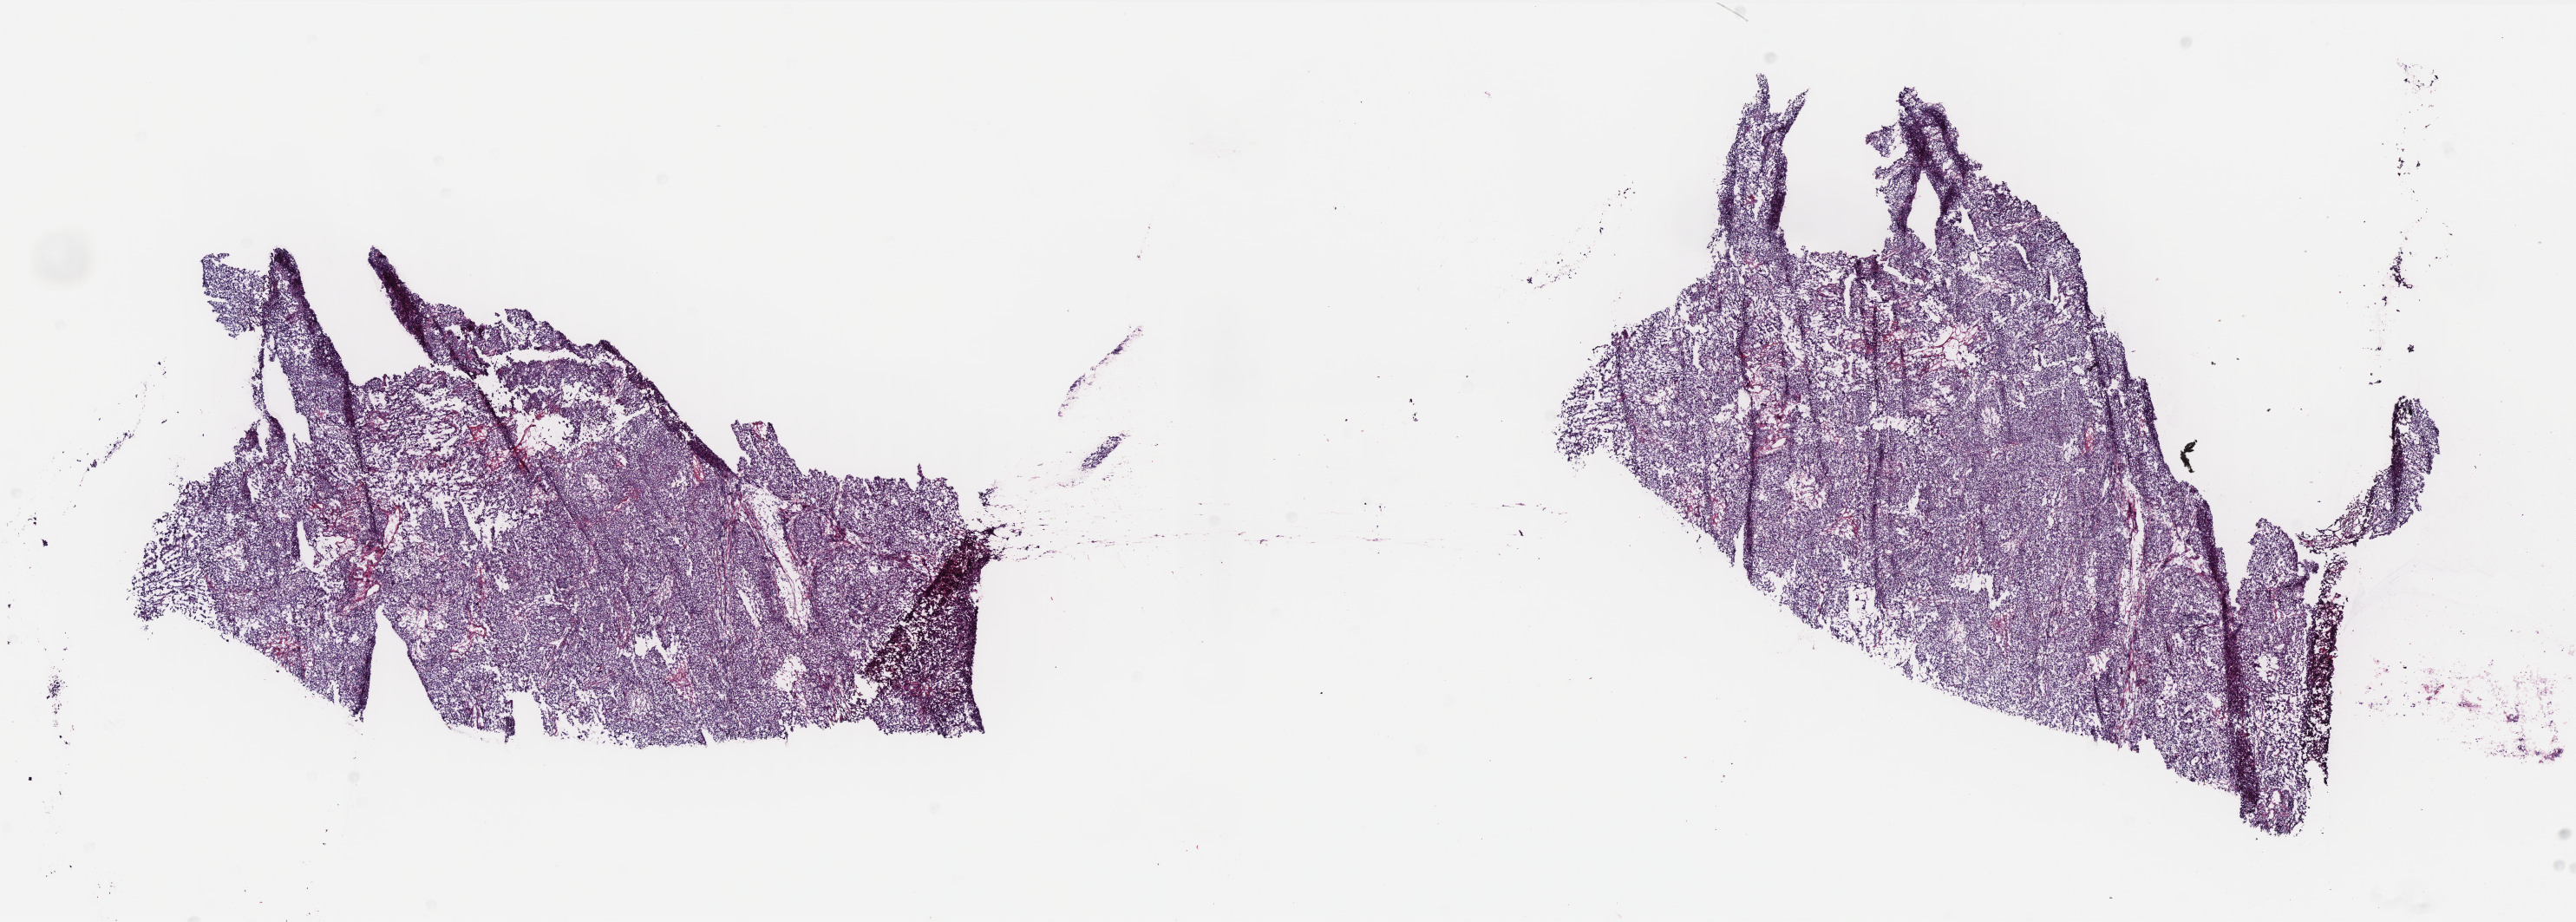
Digitized H&E-stained tissue section (whole slide), a low-resolution overview of the entire scanned area, about 23.8 x 8.5 mm. Frozen section. Uterus, primary tumour sample. Female patient; age at initial diagnosis 73 years. Histologic grade: G3 (poorly differentiated). Slide review estimates, as recorded: tumour cells 100%, tumour nuclei 75%, normal cells 0%, stromal cells 0%, necrosis 0%. Inflammatory infiltration, as recorded: lymphocyte infiltration 20%, monocyte infiltration 3%, neutrophil infiltration 0%.
* lymph nodes positive (case pathology): 0 of 21 examined
* histologic diagnosis: Clear cell adenocarcinoma, NOS (endometrium)
* FIGO stage: IB